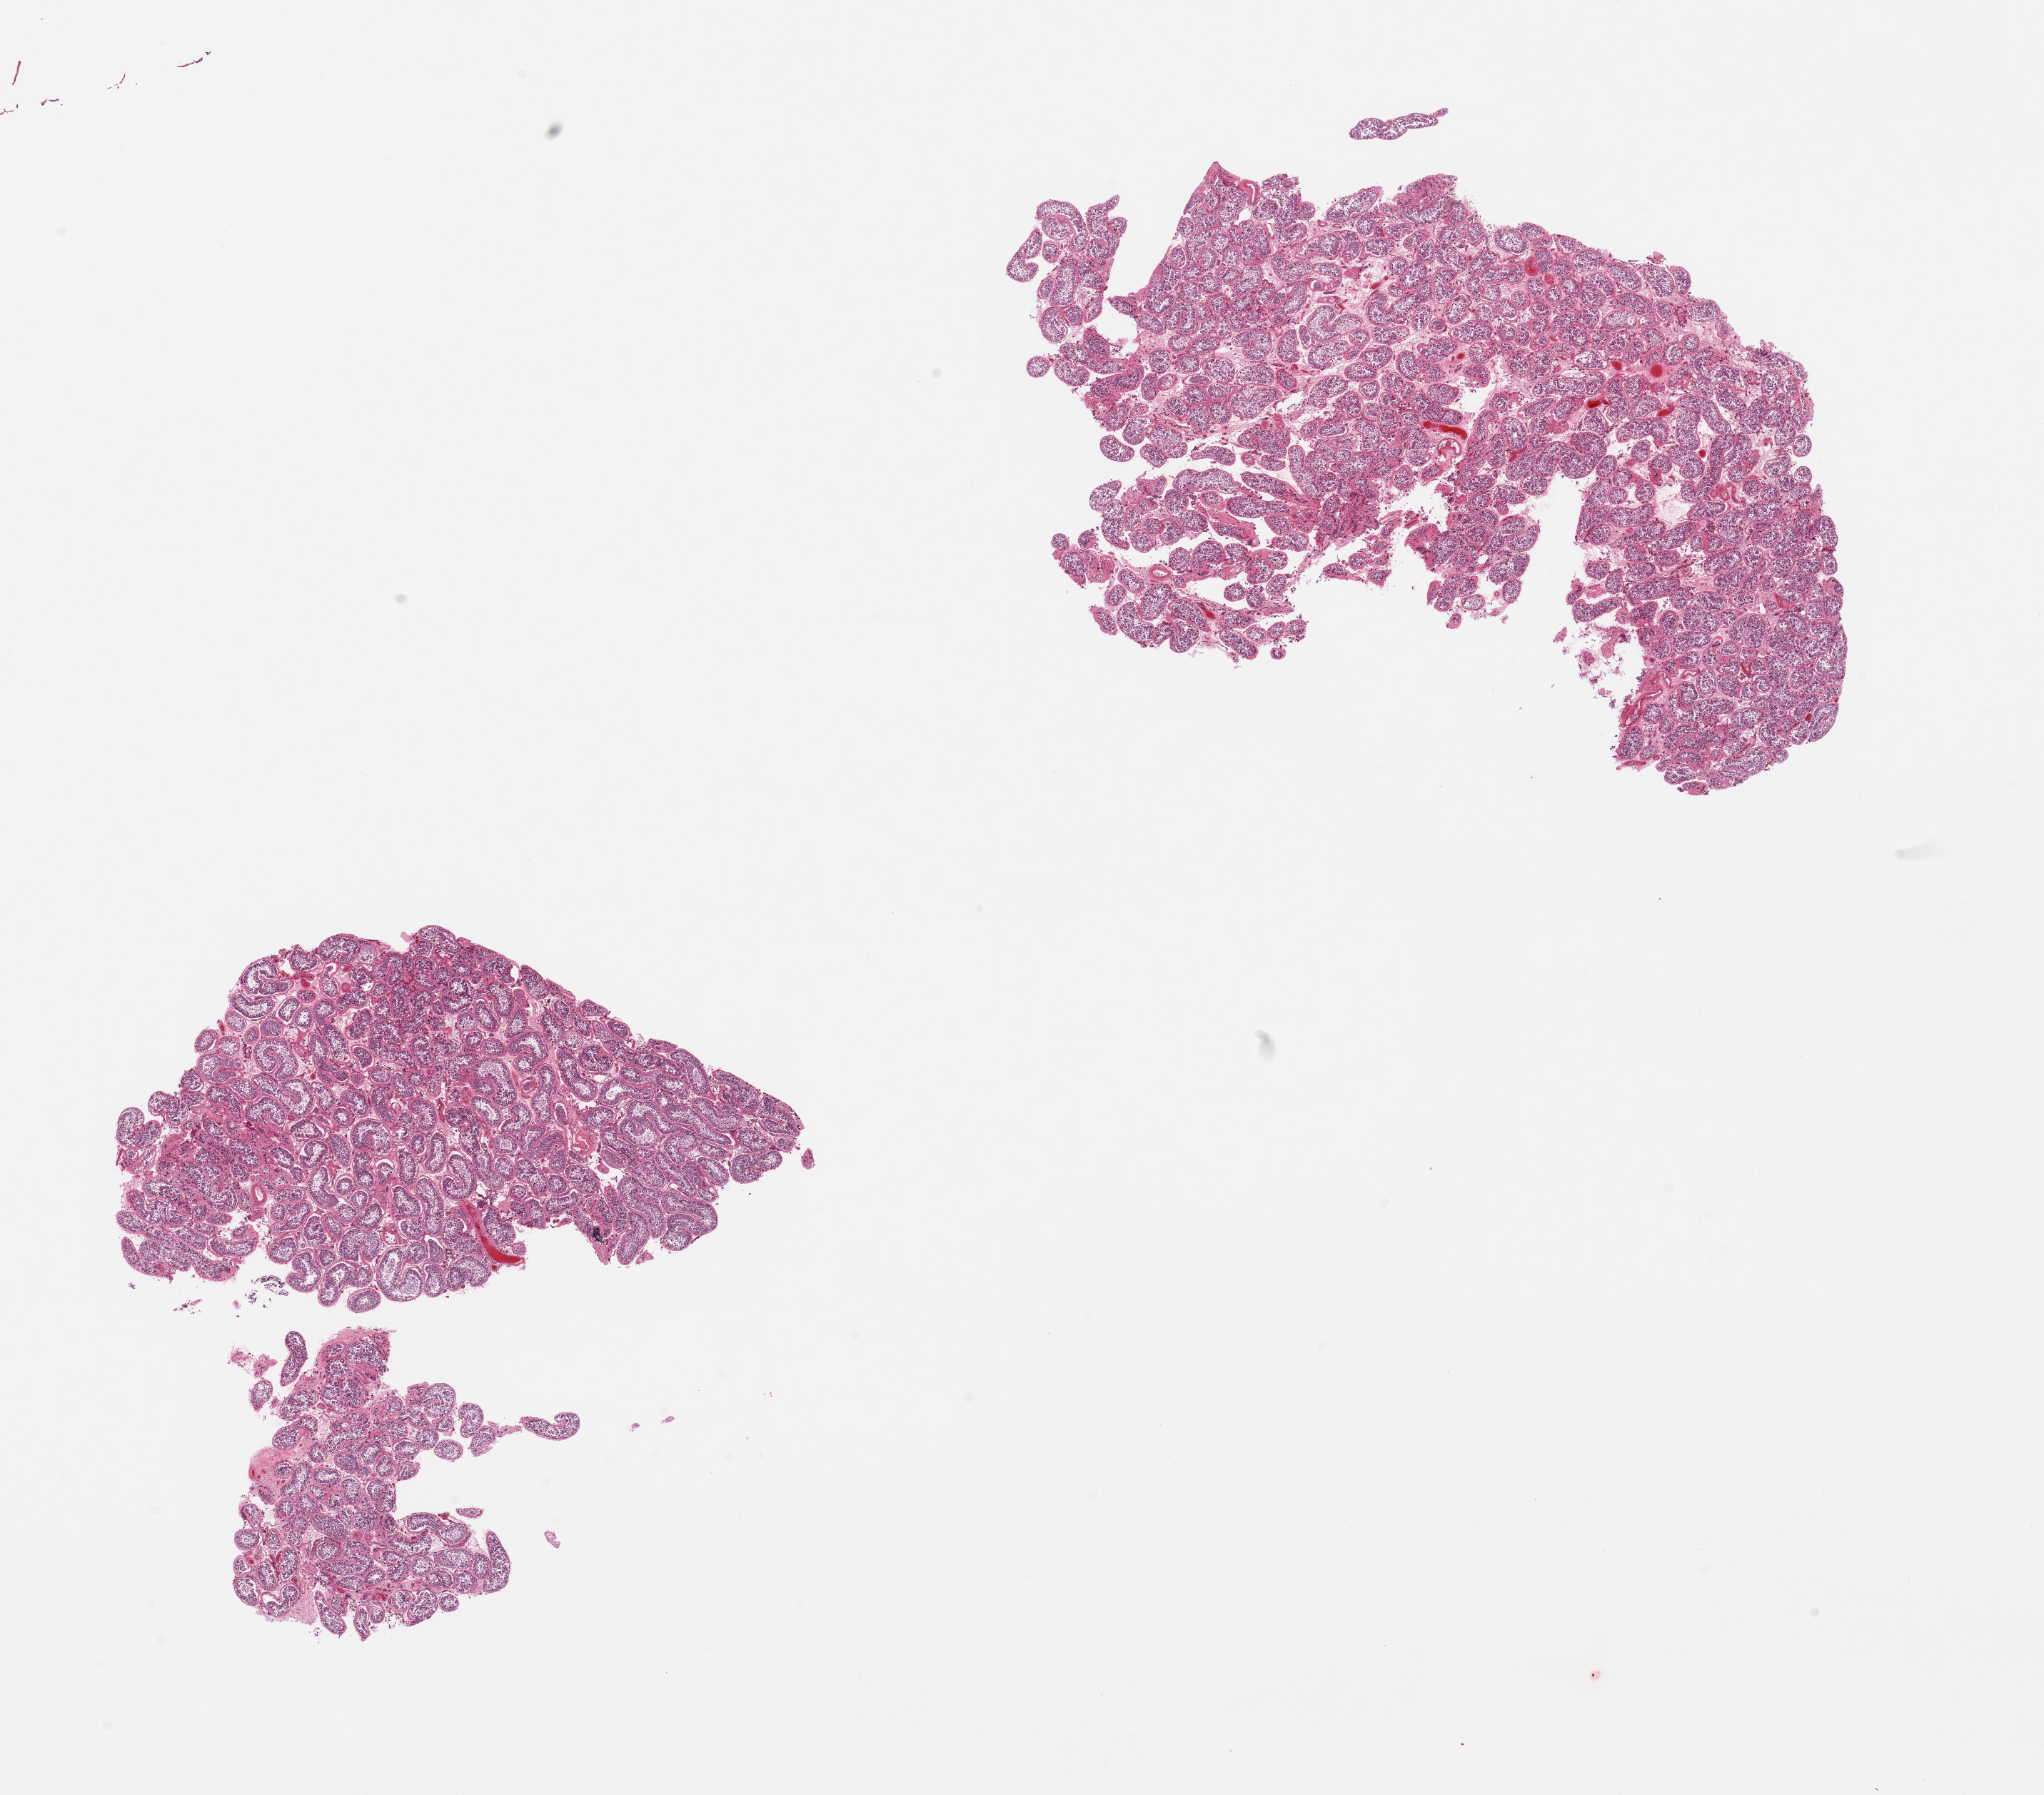
Haematoxylin and eosin whole-slide image, whole scanned area (about 22.6 x 19.9 mm, acquisition: 20x scan) shown as a low-resolution overview; PAXgene-fixed paraffin-embedded (PFPE) section; target tissue: testis; donor tissue sample. Male donor.
Pathologist's review note for this sample: 2 pieces, spermatogenesis present, increased peritubular fibrosis.